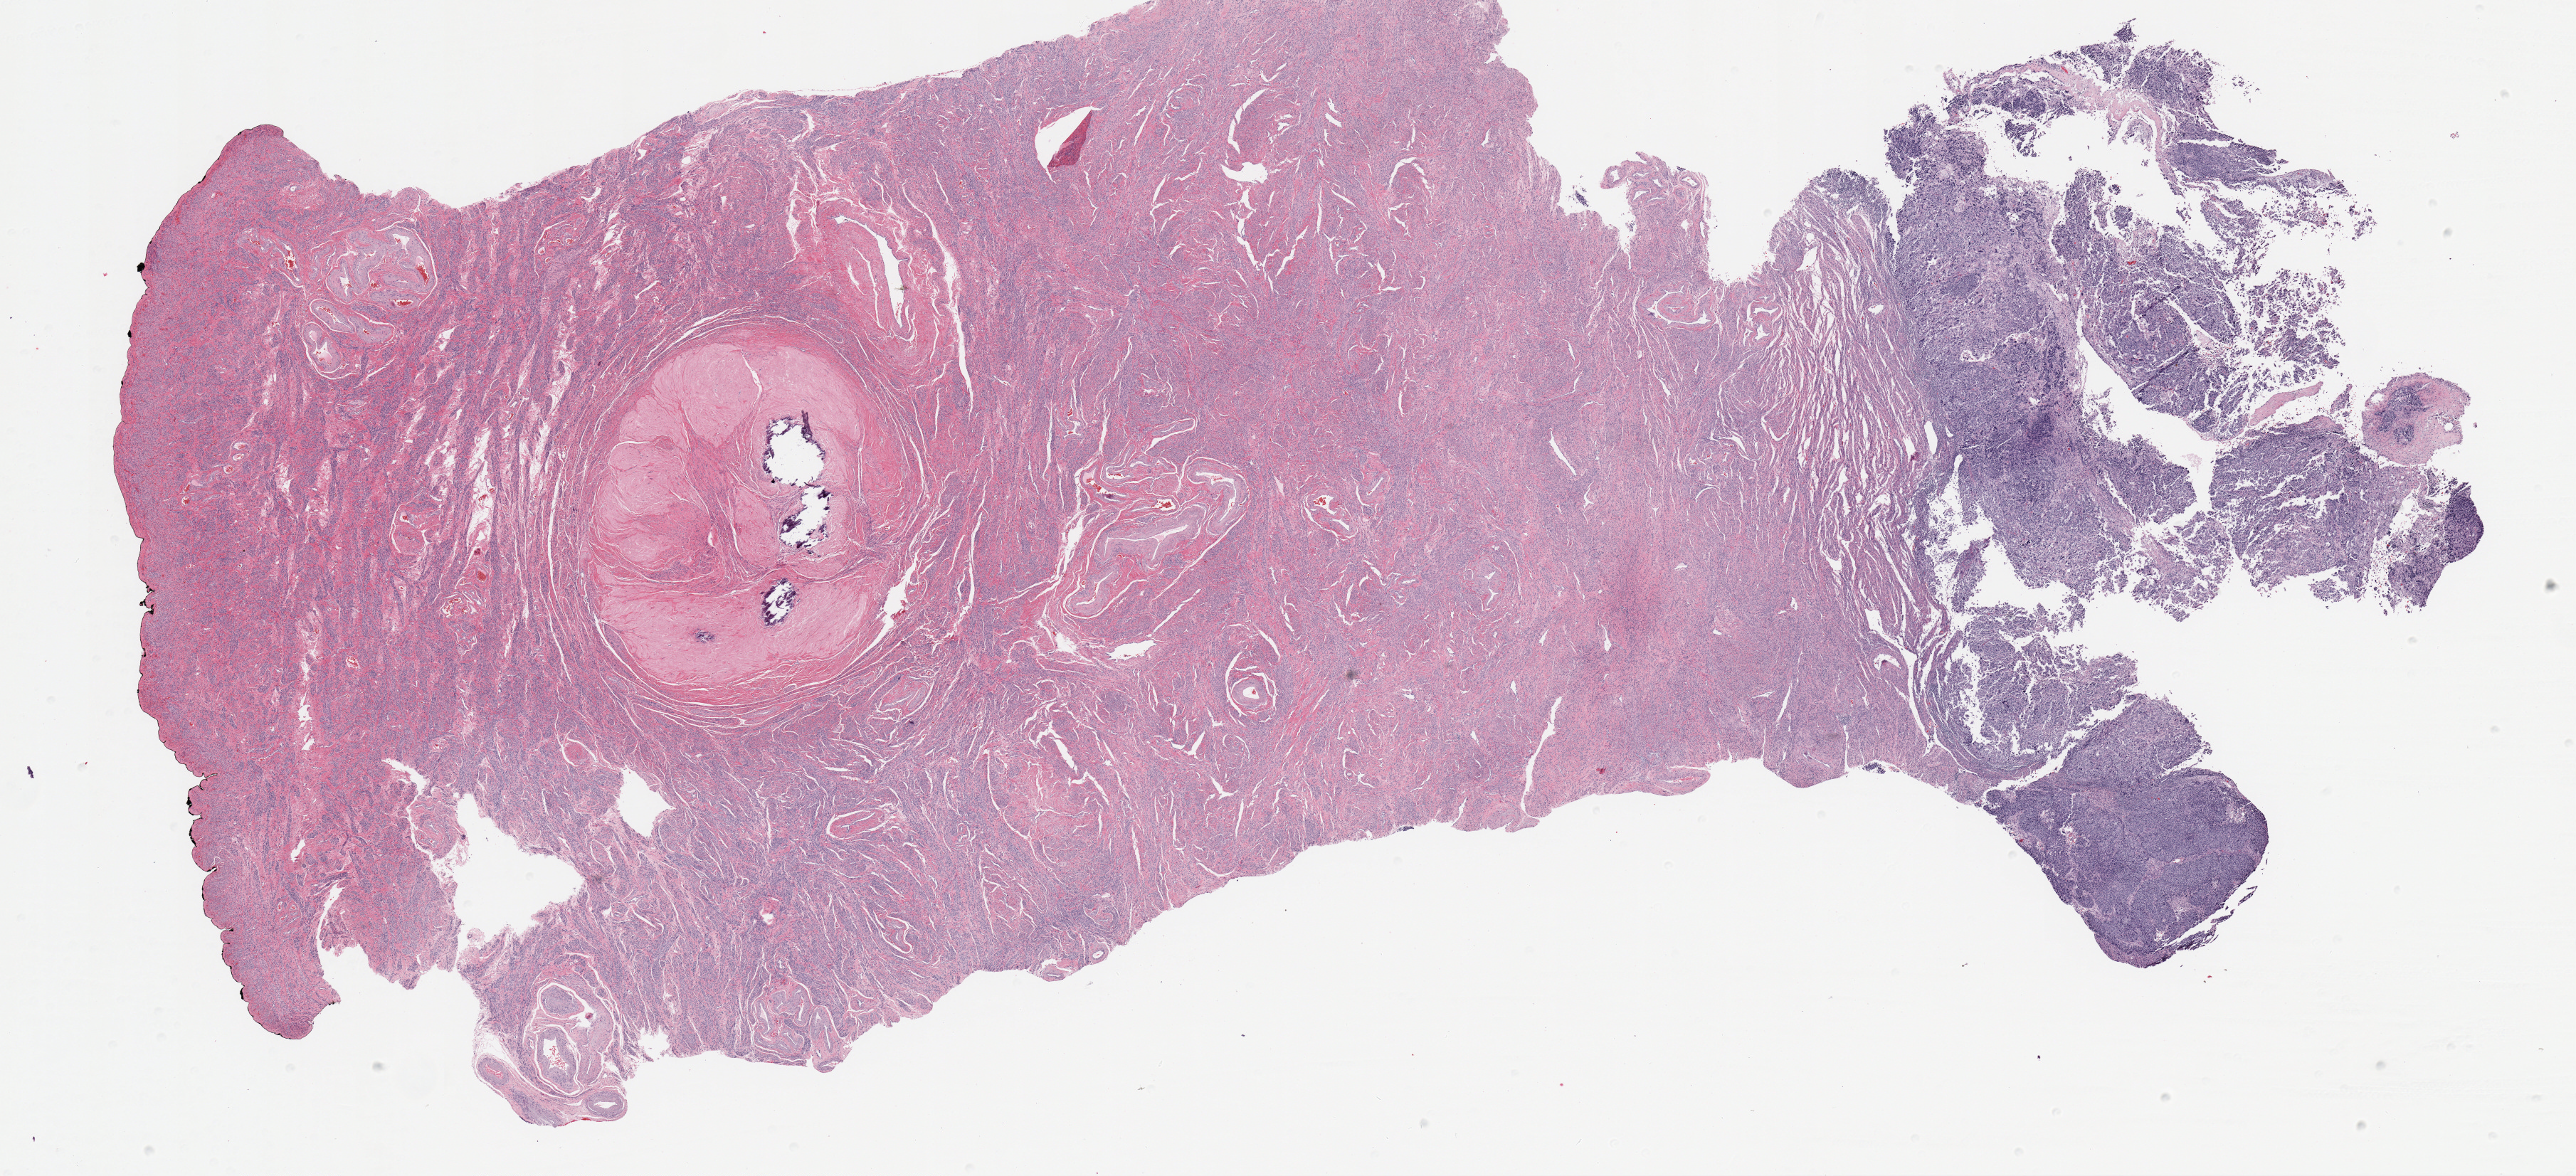
Digitized Hematoxylin and eosin (H&E) stained tissue section (whole slide) — whole scanned area (about 28.8 x 13.2 mm) shown as a low-resolution overview. Formalin-fixed paraffin-embedded (FFPE) diagnostic section. Uterus, primary tumour sample. Patient sex: female. Histologic grade: G3 (poorly differentiated).
• diagnosis: Endometrioid adenocarcinoma, NOS (endometrium)
• lymph nodes positive (case pathology): 0 of 3 examined
• FIGO stage: IA